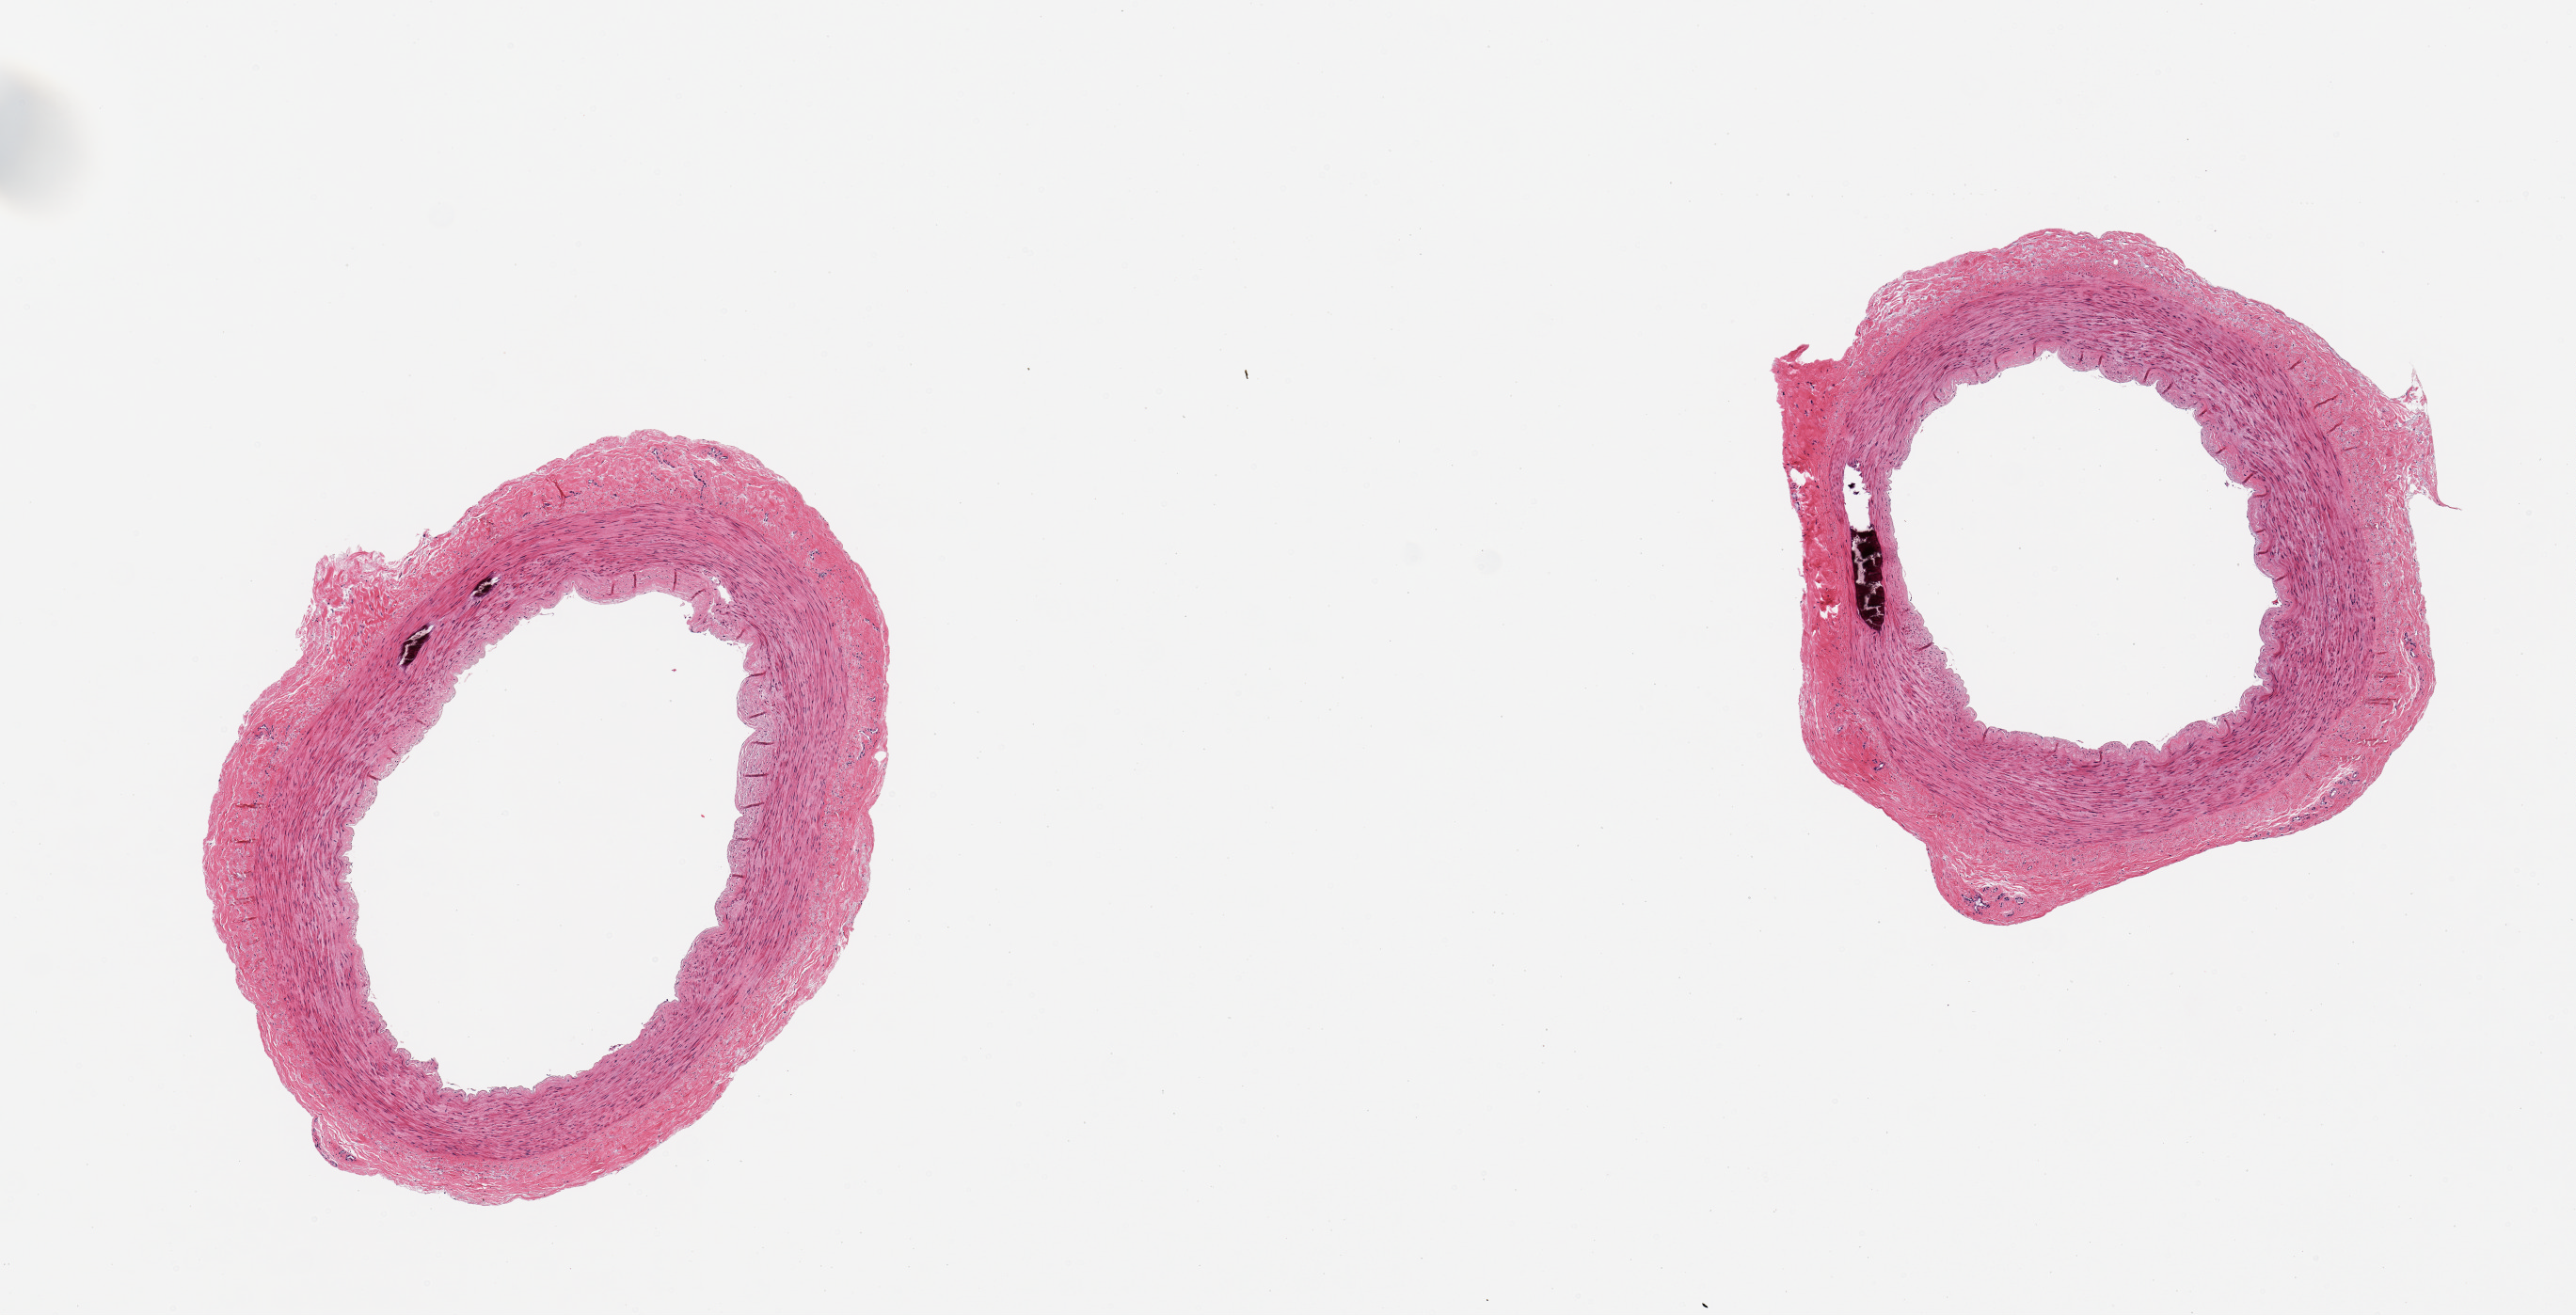
H&E whole-slide image, brightfield — low-resolution overview of the scanned area, about 10.8 x 5.5 mm; PAXgene-fixed, paraffin-embedded tissue; sampled site (target tissue): tibial artery; tissue donor sample. Donor: male.
Pathologist's review note for this sample: 2 pieces, focal Monckberg's medial sclerosis; no significant atherosis; good clean specimens.